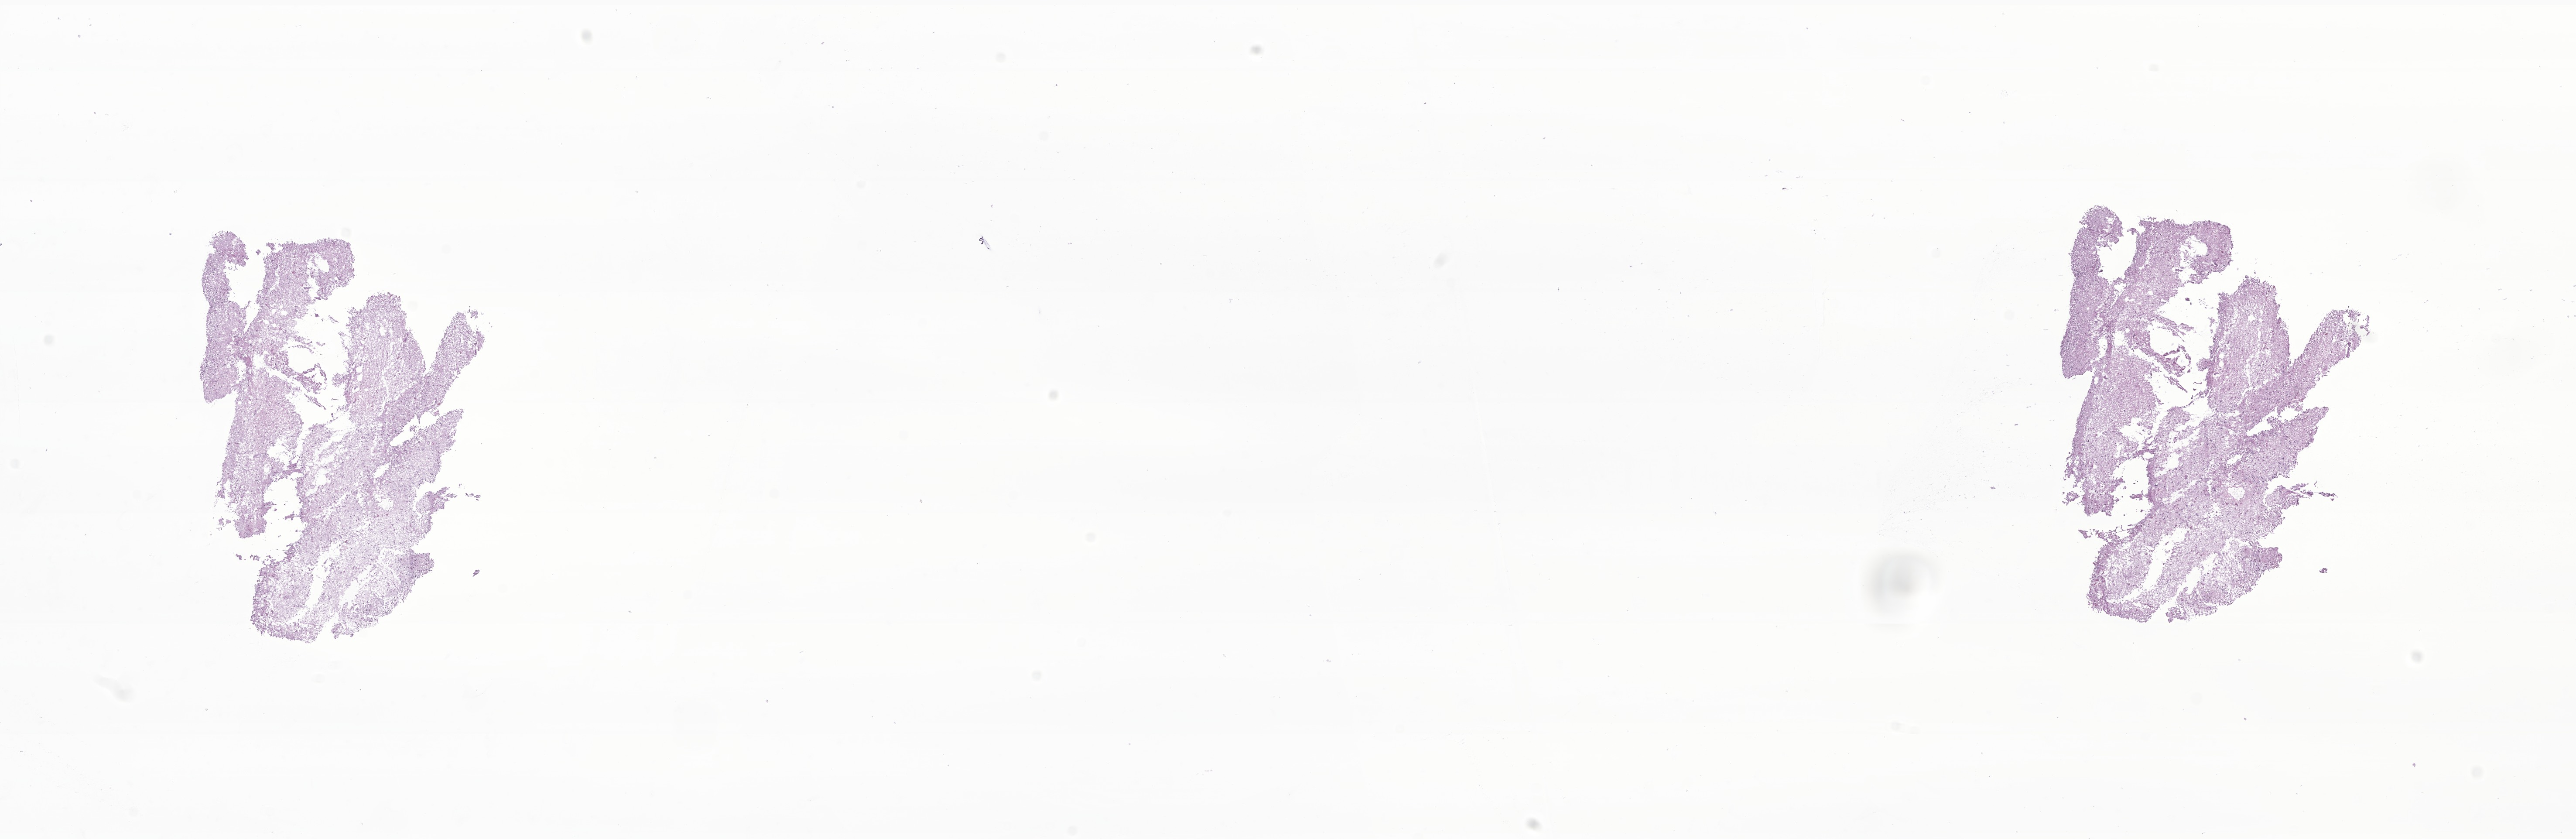
Digitized haematoxylin and eosin-stained section of tumor tissue from the brain — a low-resolution overview of the entire scanned area, about 24.9 x 8.1 mm, frozen section (OCT-embedded). Patient male; age 146 months.
- diagnosis: Pilocytic astrocytoma